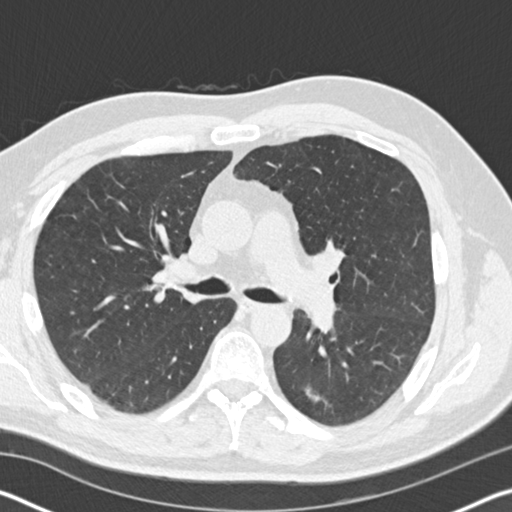
Low-dose screening chest CT, one axial slice; slice 106 of 178 in the series (ordered by position); 120 kVp; lung window (W 1500 / L -600 HU); 512 × 512 image matrix, field of view 340 × 340 mm.
Outlined on this slice (outlined manually by an expert reader):
- lesion 1 (tumor, lower lobe of left lung): box from (x=305, y=387) to (x=326, y=403) px